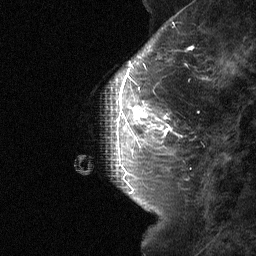
Breast MRI (dynamic contrast-enhanced), one sagittal slice; dynamic contrast-enhanced study with each time point stored as its own series, time point 2 of 3 at this slice position (early post-contrast, ordered by acquisition time); 1.5 T; TE 4.8 ms, TR 27 ms; 256 × 256 image matrix, field of view 180 × 180 mm. Patient: female, 42 years. Case-level facts recorded for this patient, not image findings: setting: breast cancer imaged before/during neoadjuvant chemotherapy; receptor status: triple-negative.
Outlined on this slice (semi-automatically segmented with operator editing):
- analysis volume of interest (the breast-tissue region the enhancement analysis was run in; not a lesion): bounding box [x1, y1, x2, y2] px = [115, 85, 183, 160]
- tumour enhancement mask (voxels above the 90 % enhancement threshold inside the analysis volume of interest): [120, 88, 168, 138]